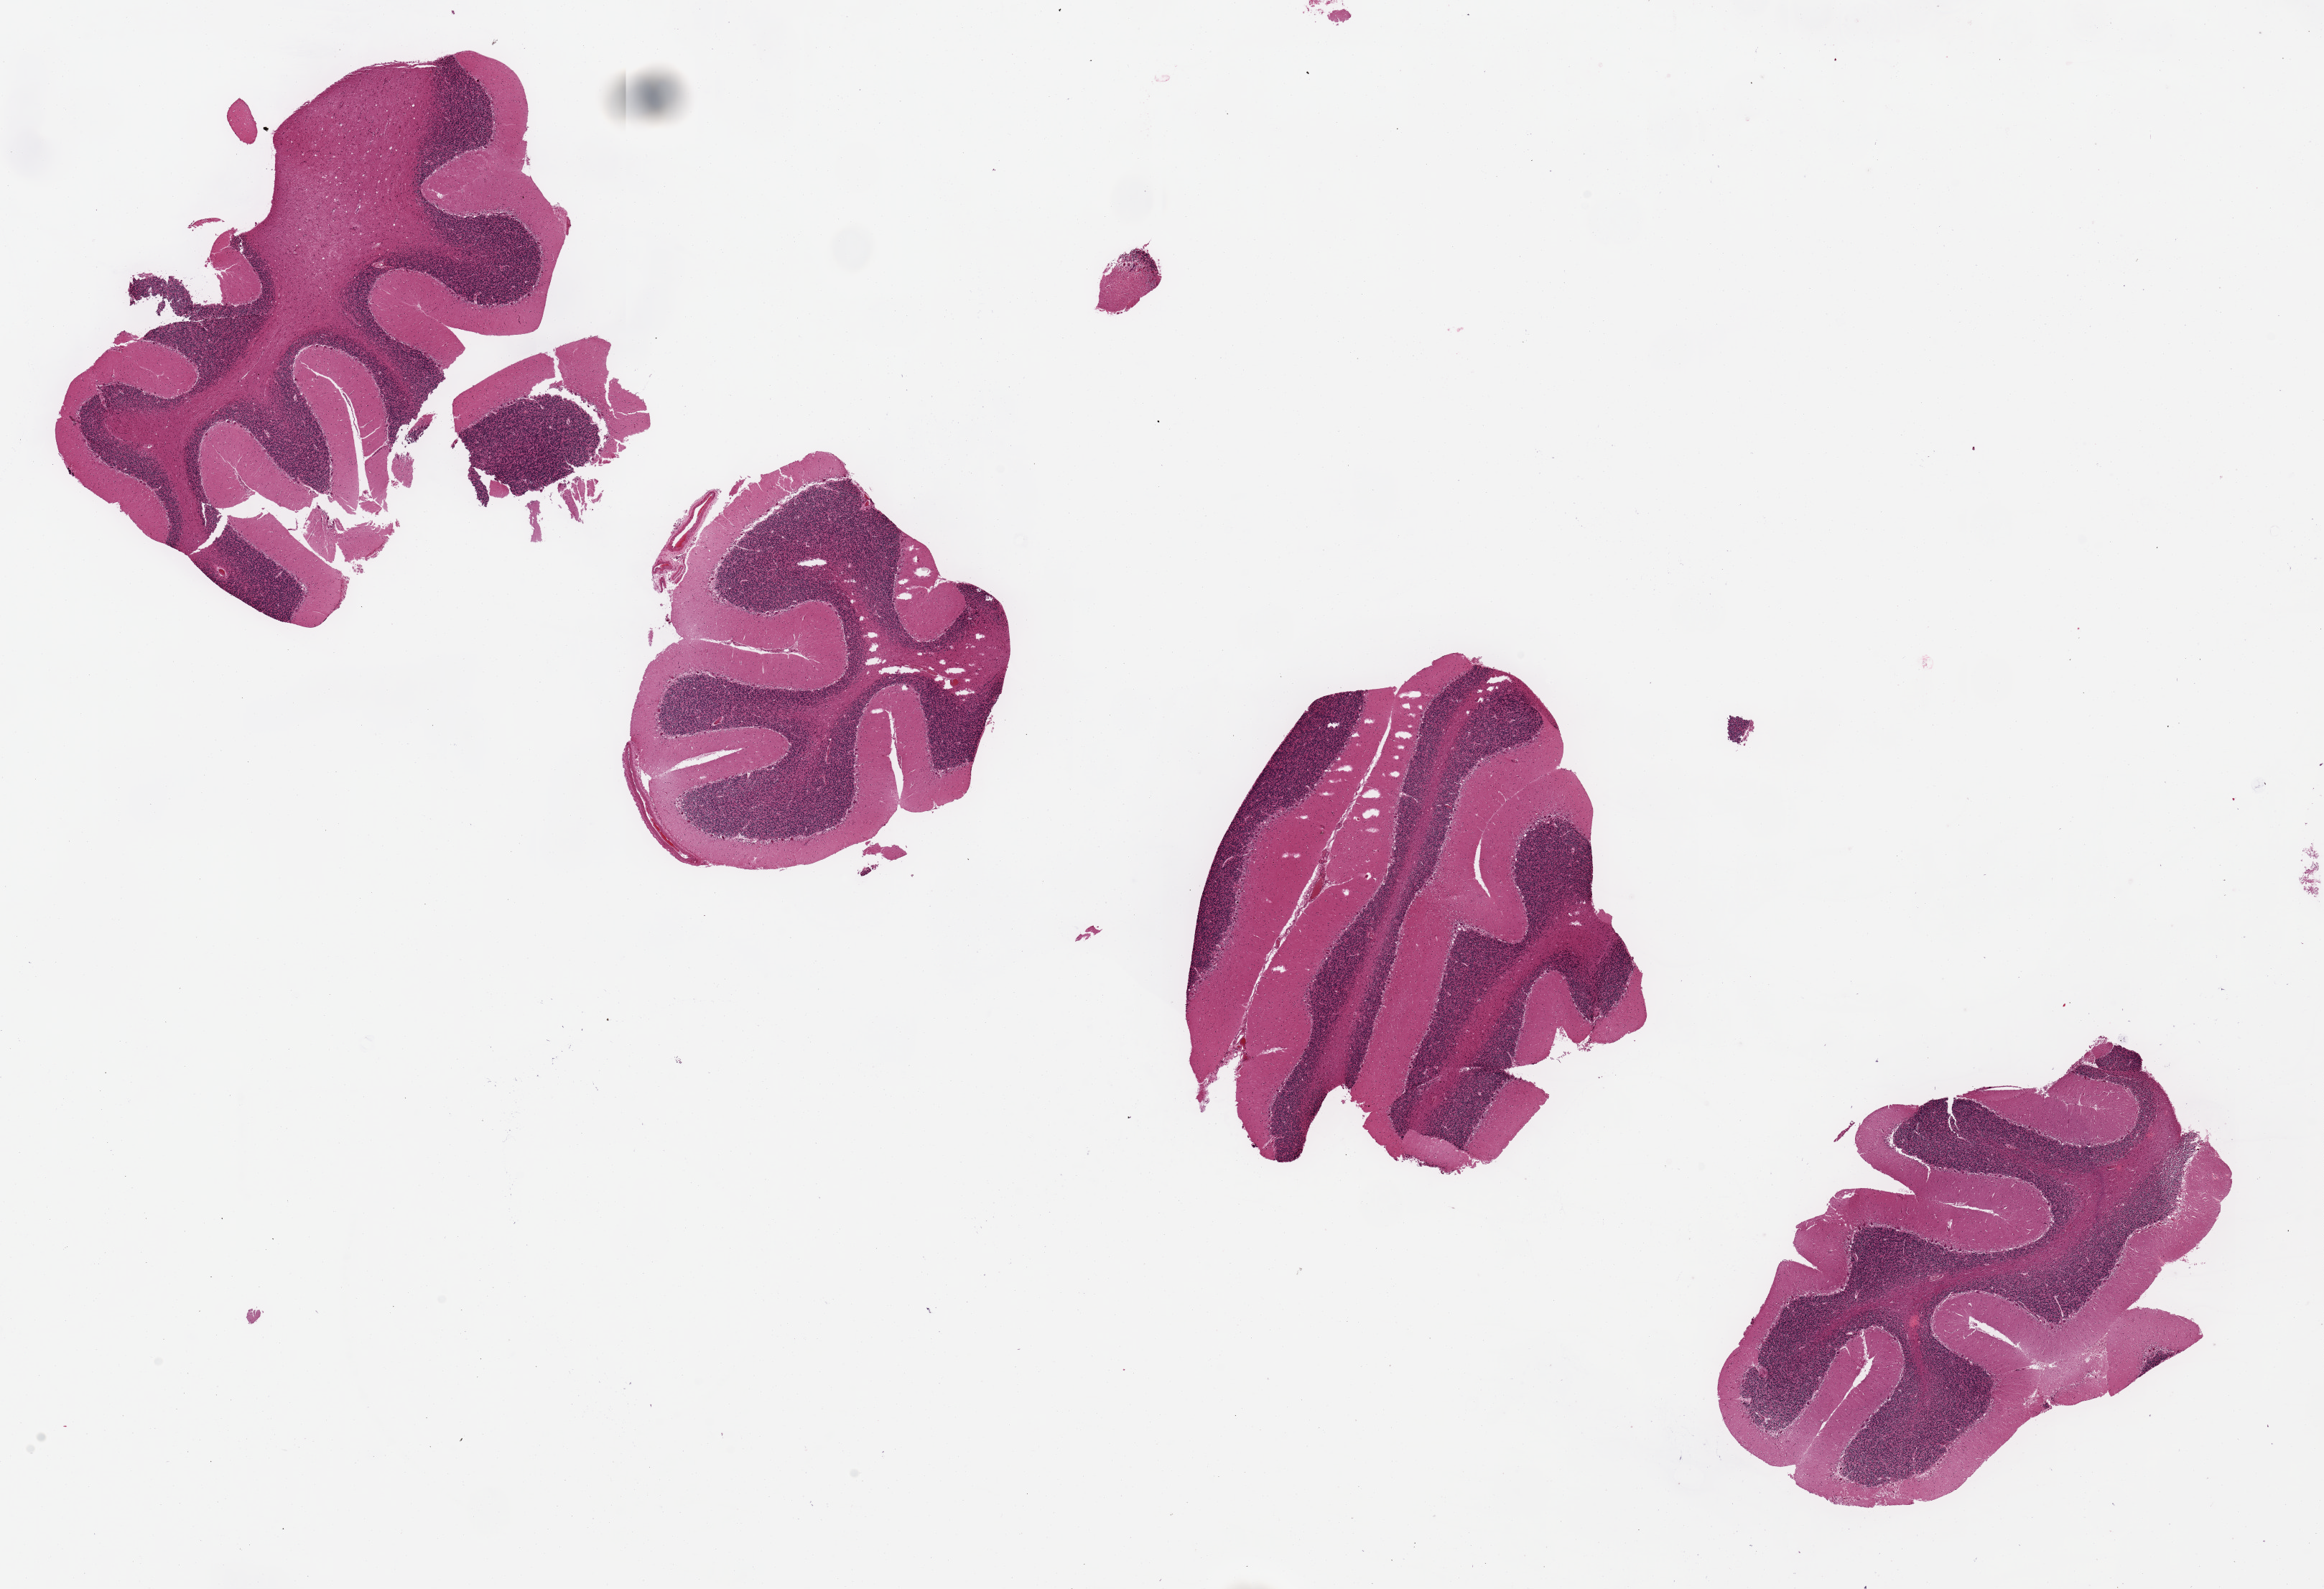
Digitized hematoxylin and eosin (H&E)-stained section — whole scanned area (about 25.6 x 17.5 mm, from a 20x scan) shown as a low-resolution overview; PAXgene-fixed paraffin-embedded (PFPE) section; section of cerebellum (target tissue); tissue donor sample. Male donor.
* reviewer comment on this tissue sample: 4 pieces, ~6x3 mm; moderate tissue tears